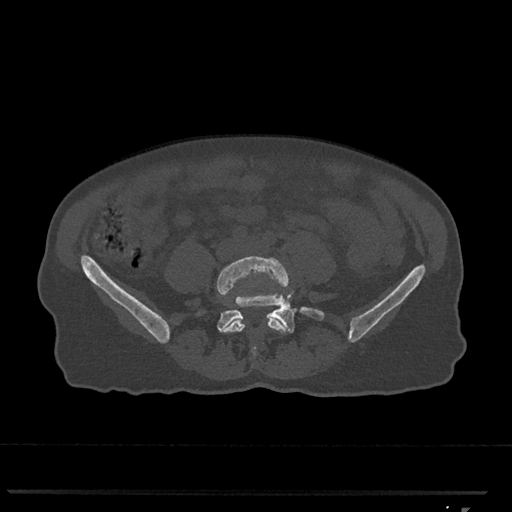
CT including the spine, one axial slice; position 177 of 793 along the scan axis; reconstruction kernel Br40s/3; 120 kVp; bone window (W 1800 / L 400 HU); 0.5 mm slice thickness; 512 × 512 image matrix, field of view 380 × 380 mm. Patient: female, 62 years. From the clinical record (not read from this slice): primary cancer: renal.
Annotated regions visible in this slice (semi-automatically segmented with operator editing):
- L4 vertebra: bounding box <217,256,289,355> (left, top, right, bottom; pixels)
- L5 vertebra: <217,283,325,333>